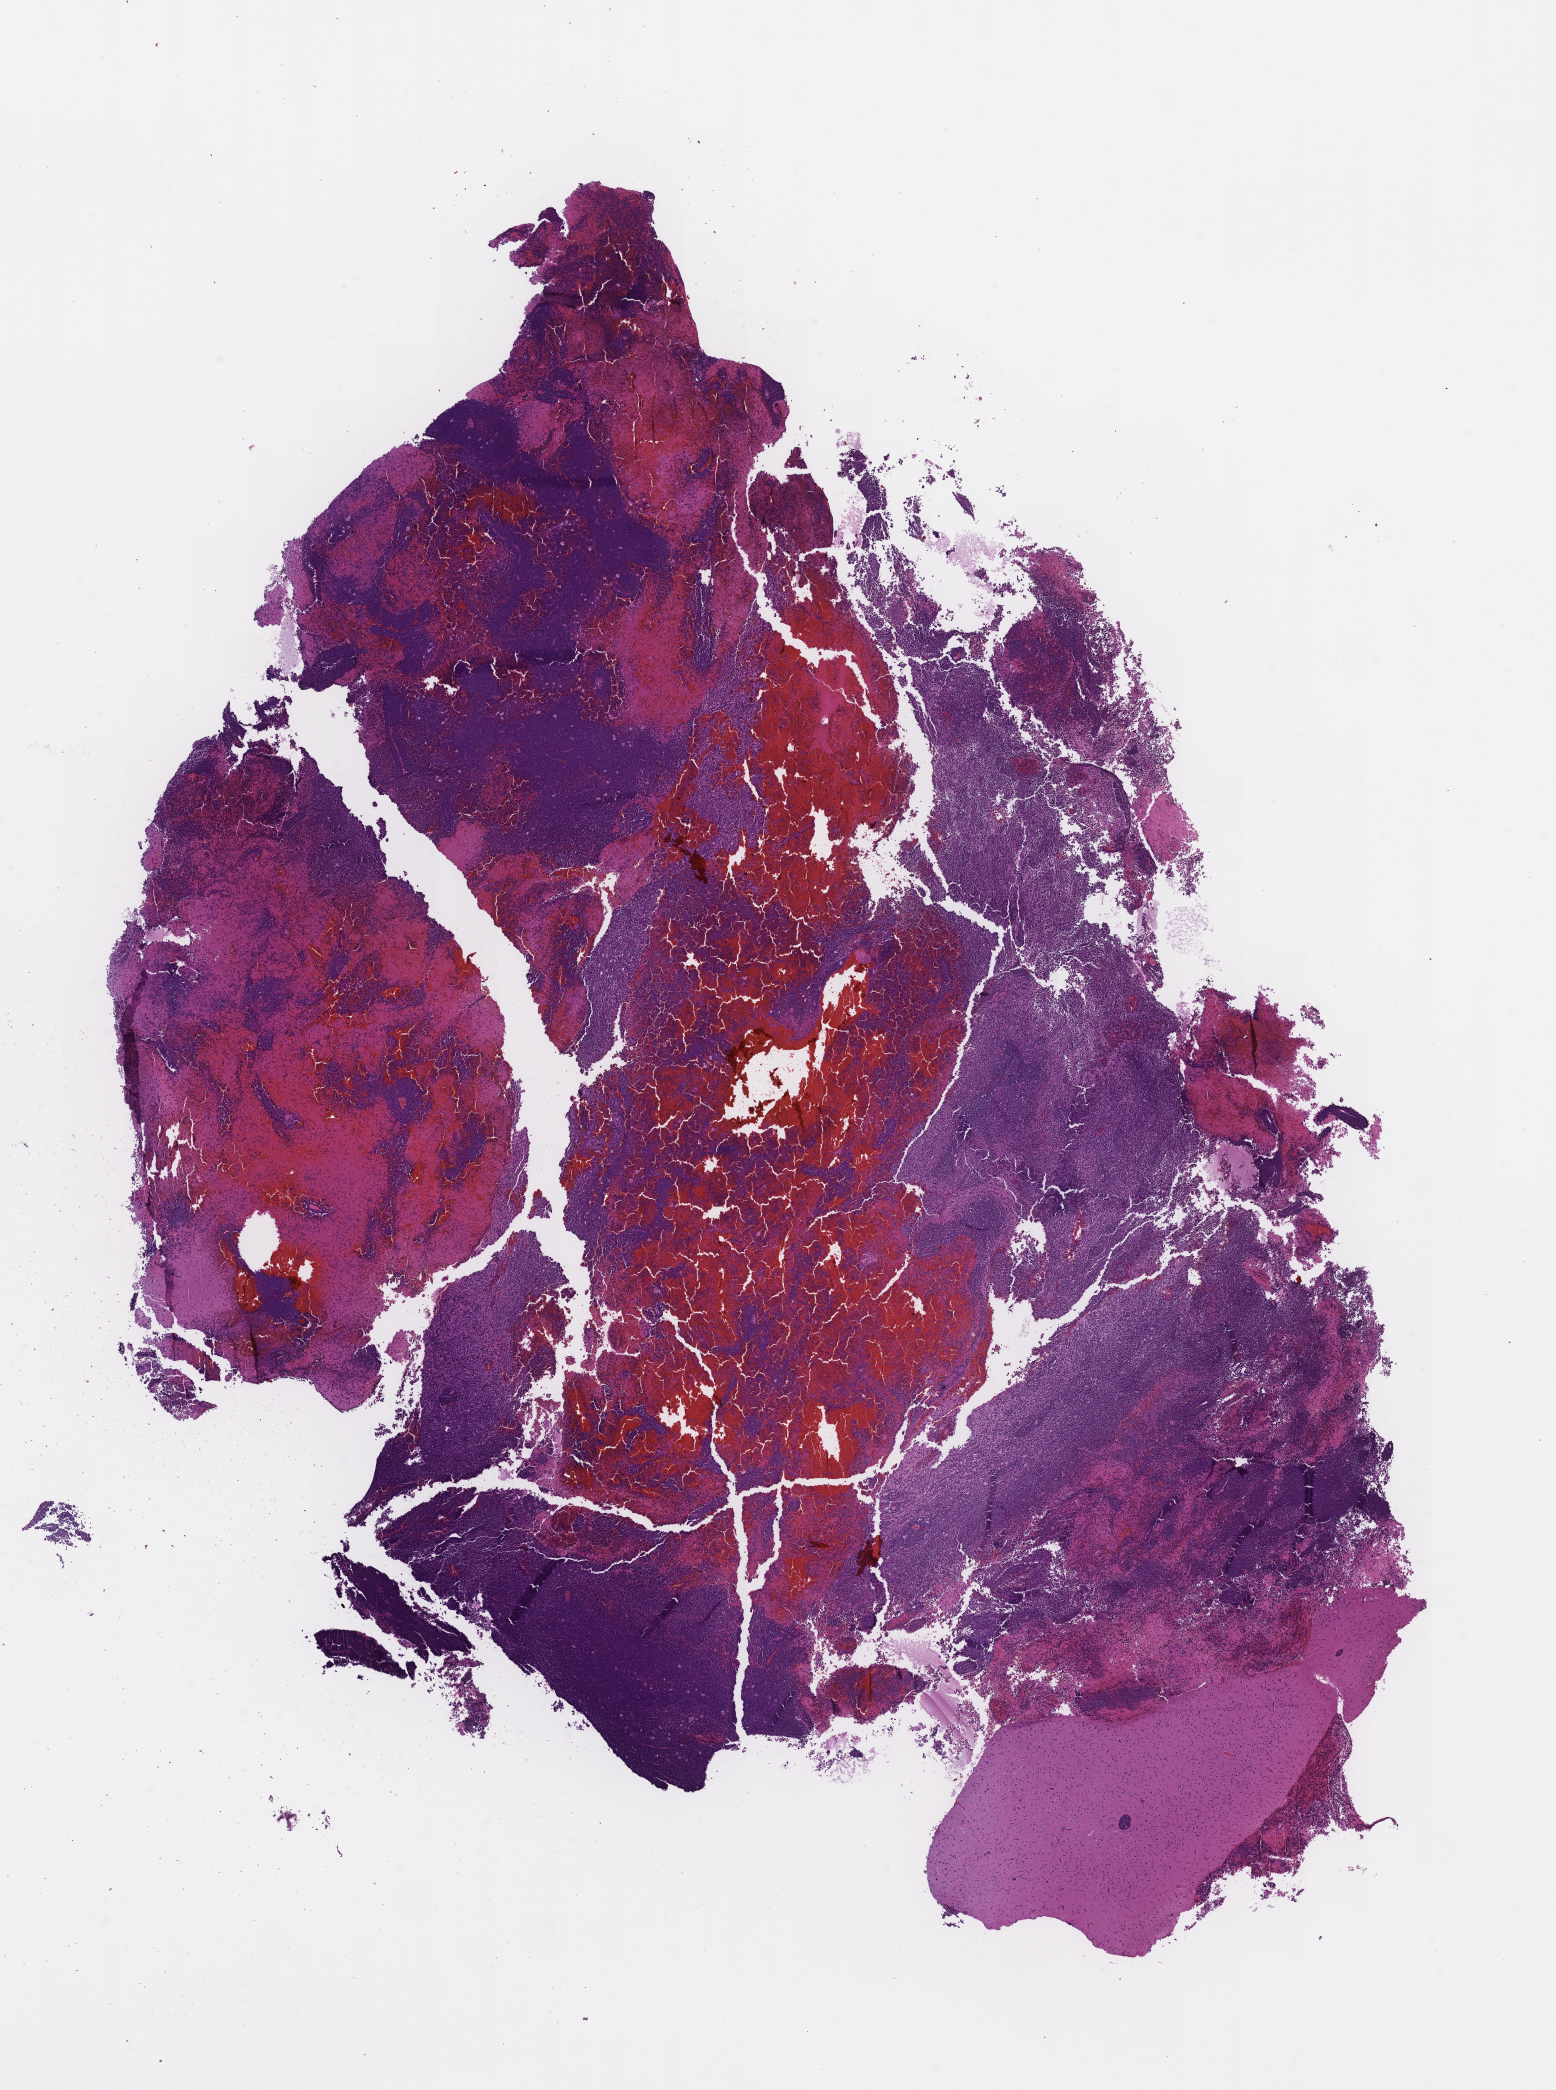
Whole-slide image, hematoxylin and eosin (H&E) stain — low-resolution overview of the scanned area, about 12.6 x 16.9 mm; FFPE section; collected at disease progression. Female patient.
• this section: metastasis (sampled organ not recorded)
• patient diagnosis (primary): Acute Myeloid Leukemia Not Otherwise Specified